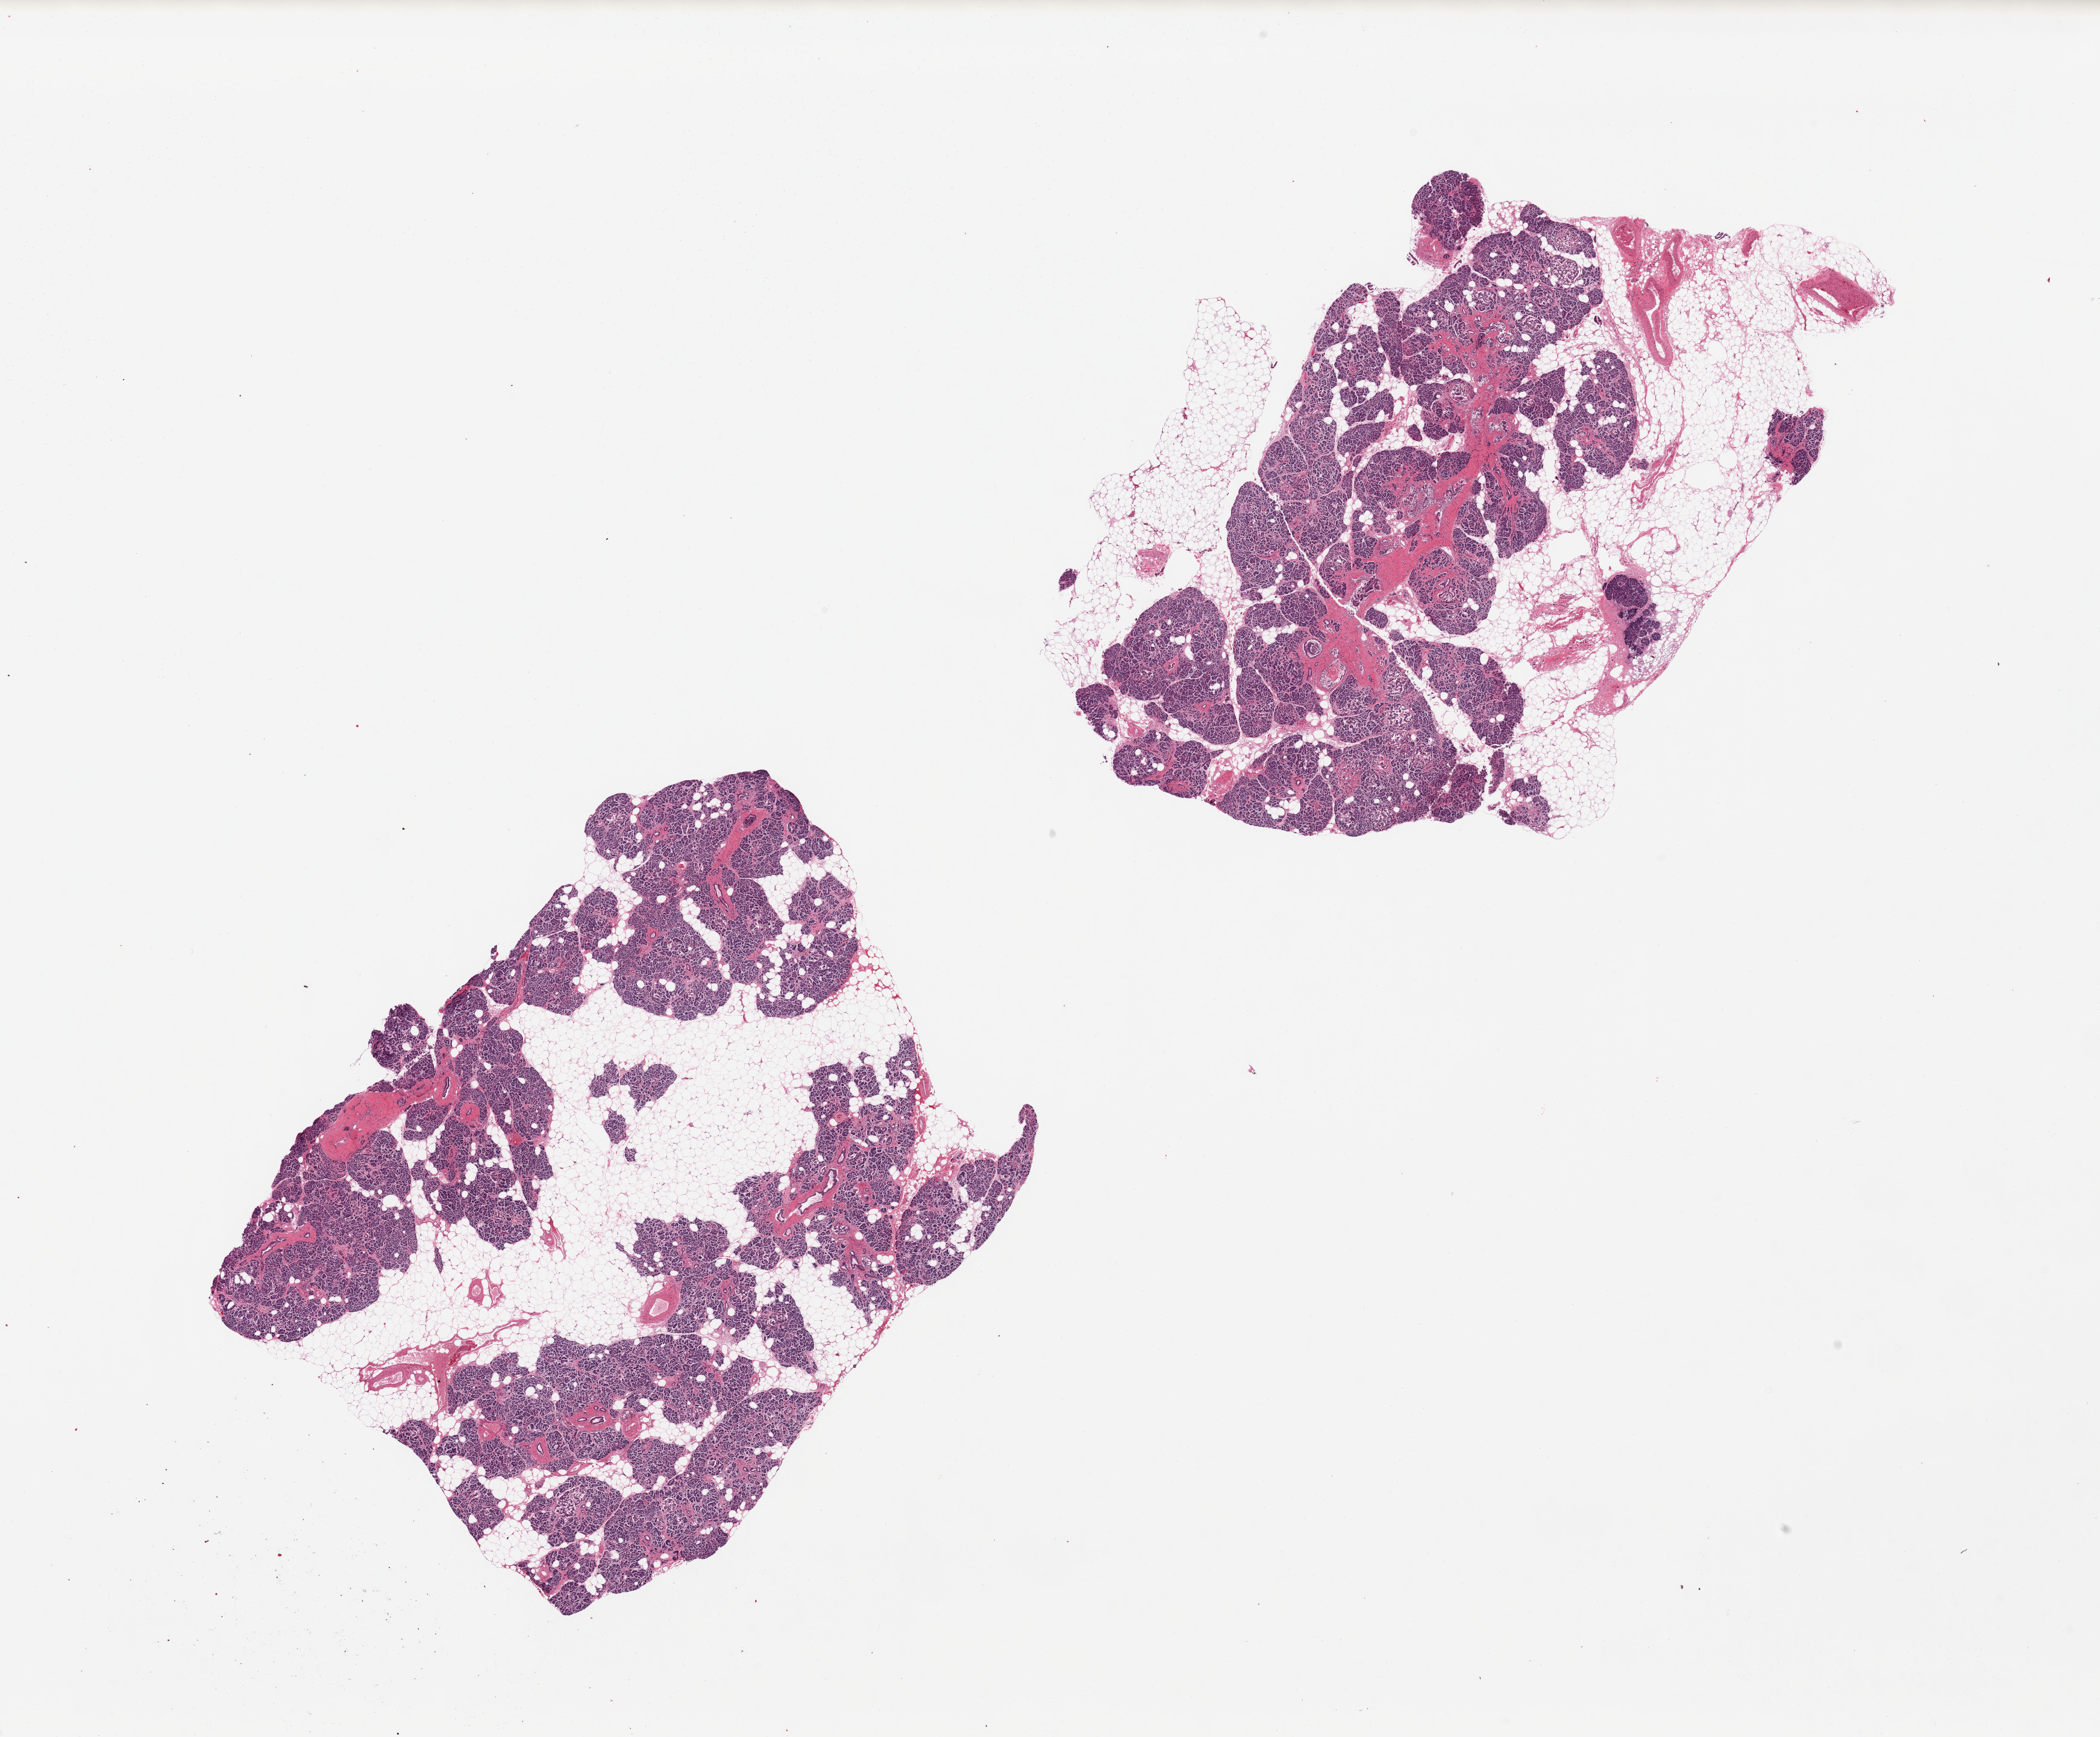
Digitized haematoxylin and eosin-stained section, low-resolution overview of the scanned area, about 27.6 x 22.8 mm, PAXgene-fixed, paraffin-embedded tissue, target tissue: pancreas, donor tissue sample.
• pathologist's review note for this sample: 2 pieces; 40% internal and external fat